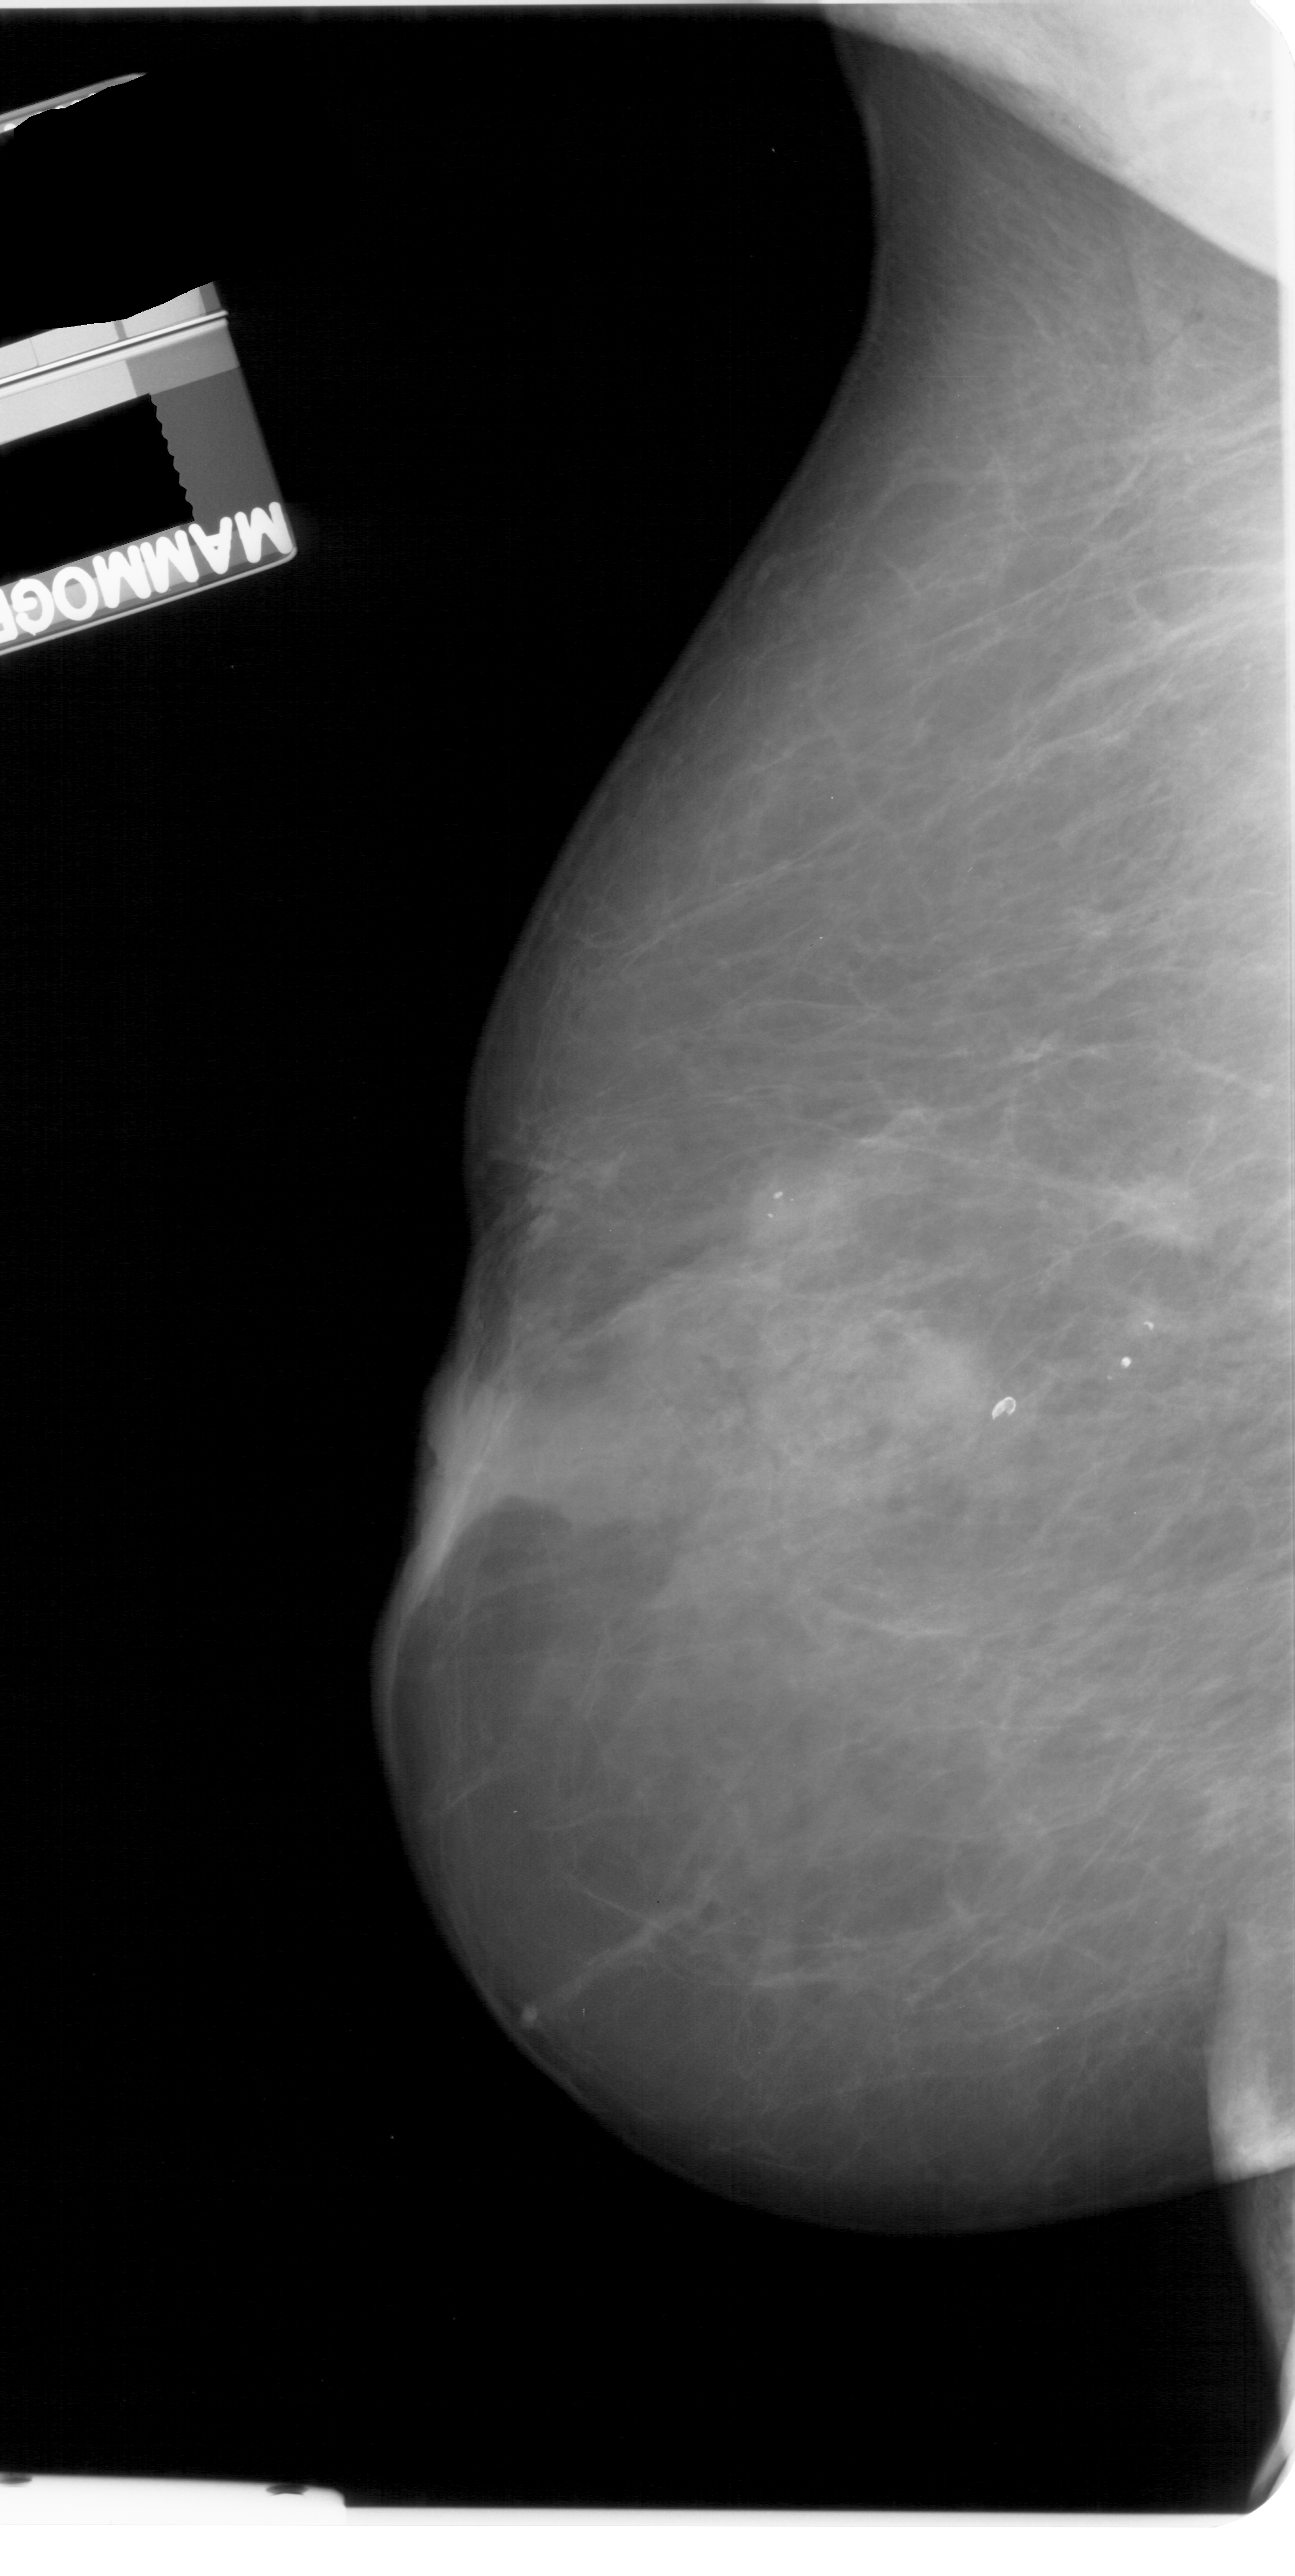
Scanned film-screen mammogram. Left breast. MLO view. BI-RADS breast density category 4 (scale 1–4). 1295 × 2576 image matrix.
Marked abnormalities (boxes around the expert regions of interest):
- mass, shape oval, margins spiculated; BI-RADS assessment category 4; subtlety rating 3 on a 1 (subtle) to 5 (obvious) scale; pathology (as recorded): malignant: bounding box [x1, y1, x2, y2] px = [1098, 1162, 1205, 1257]